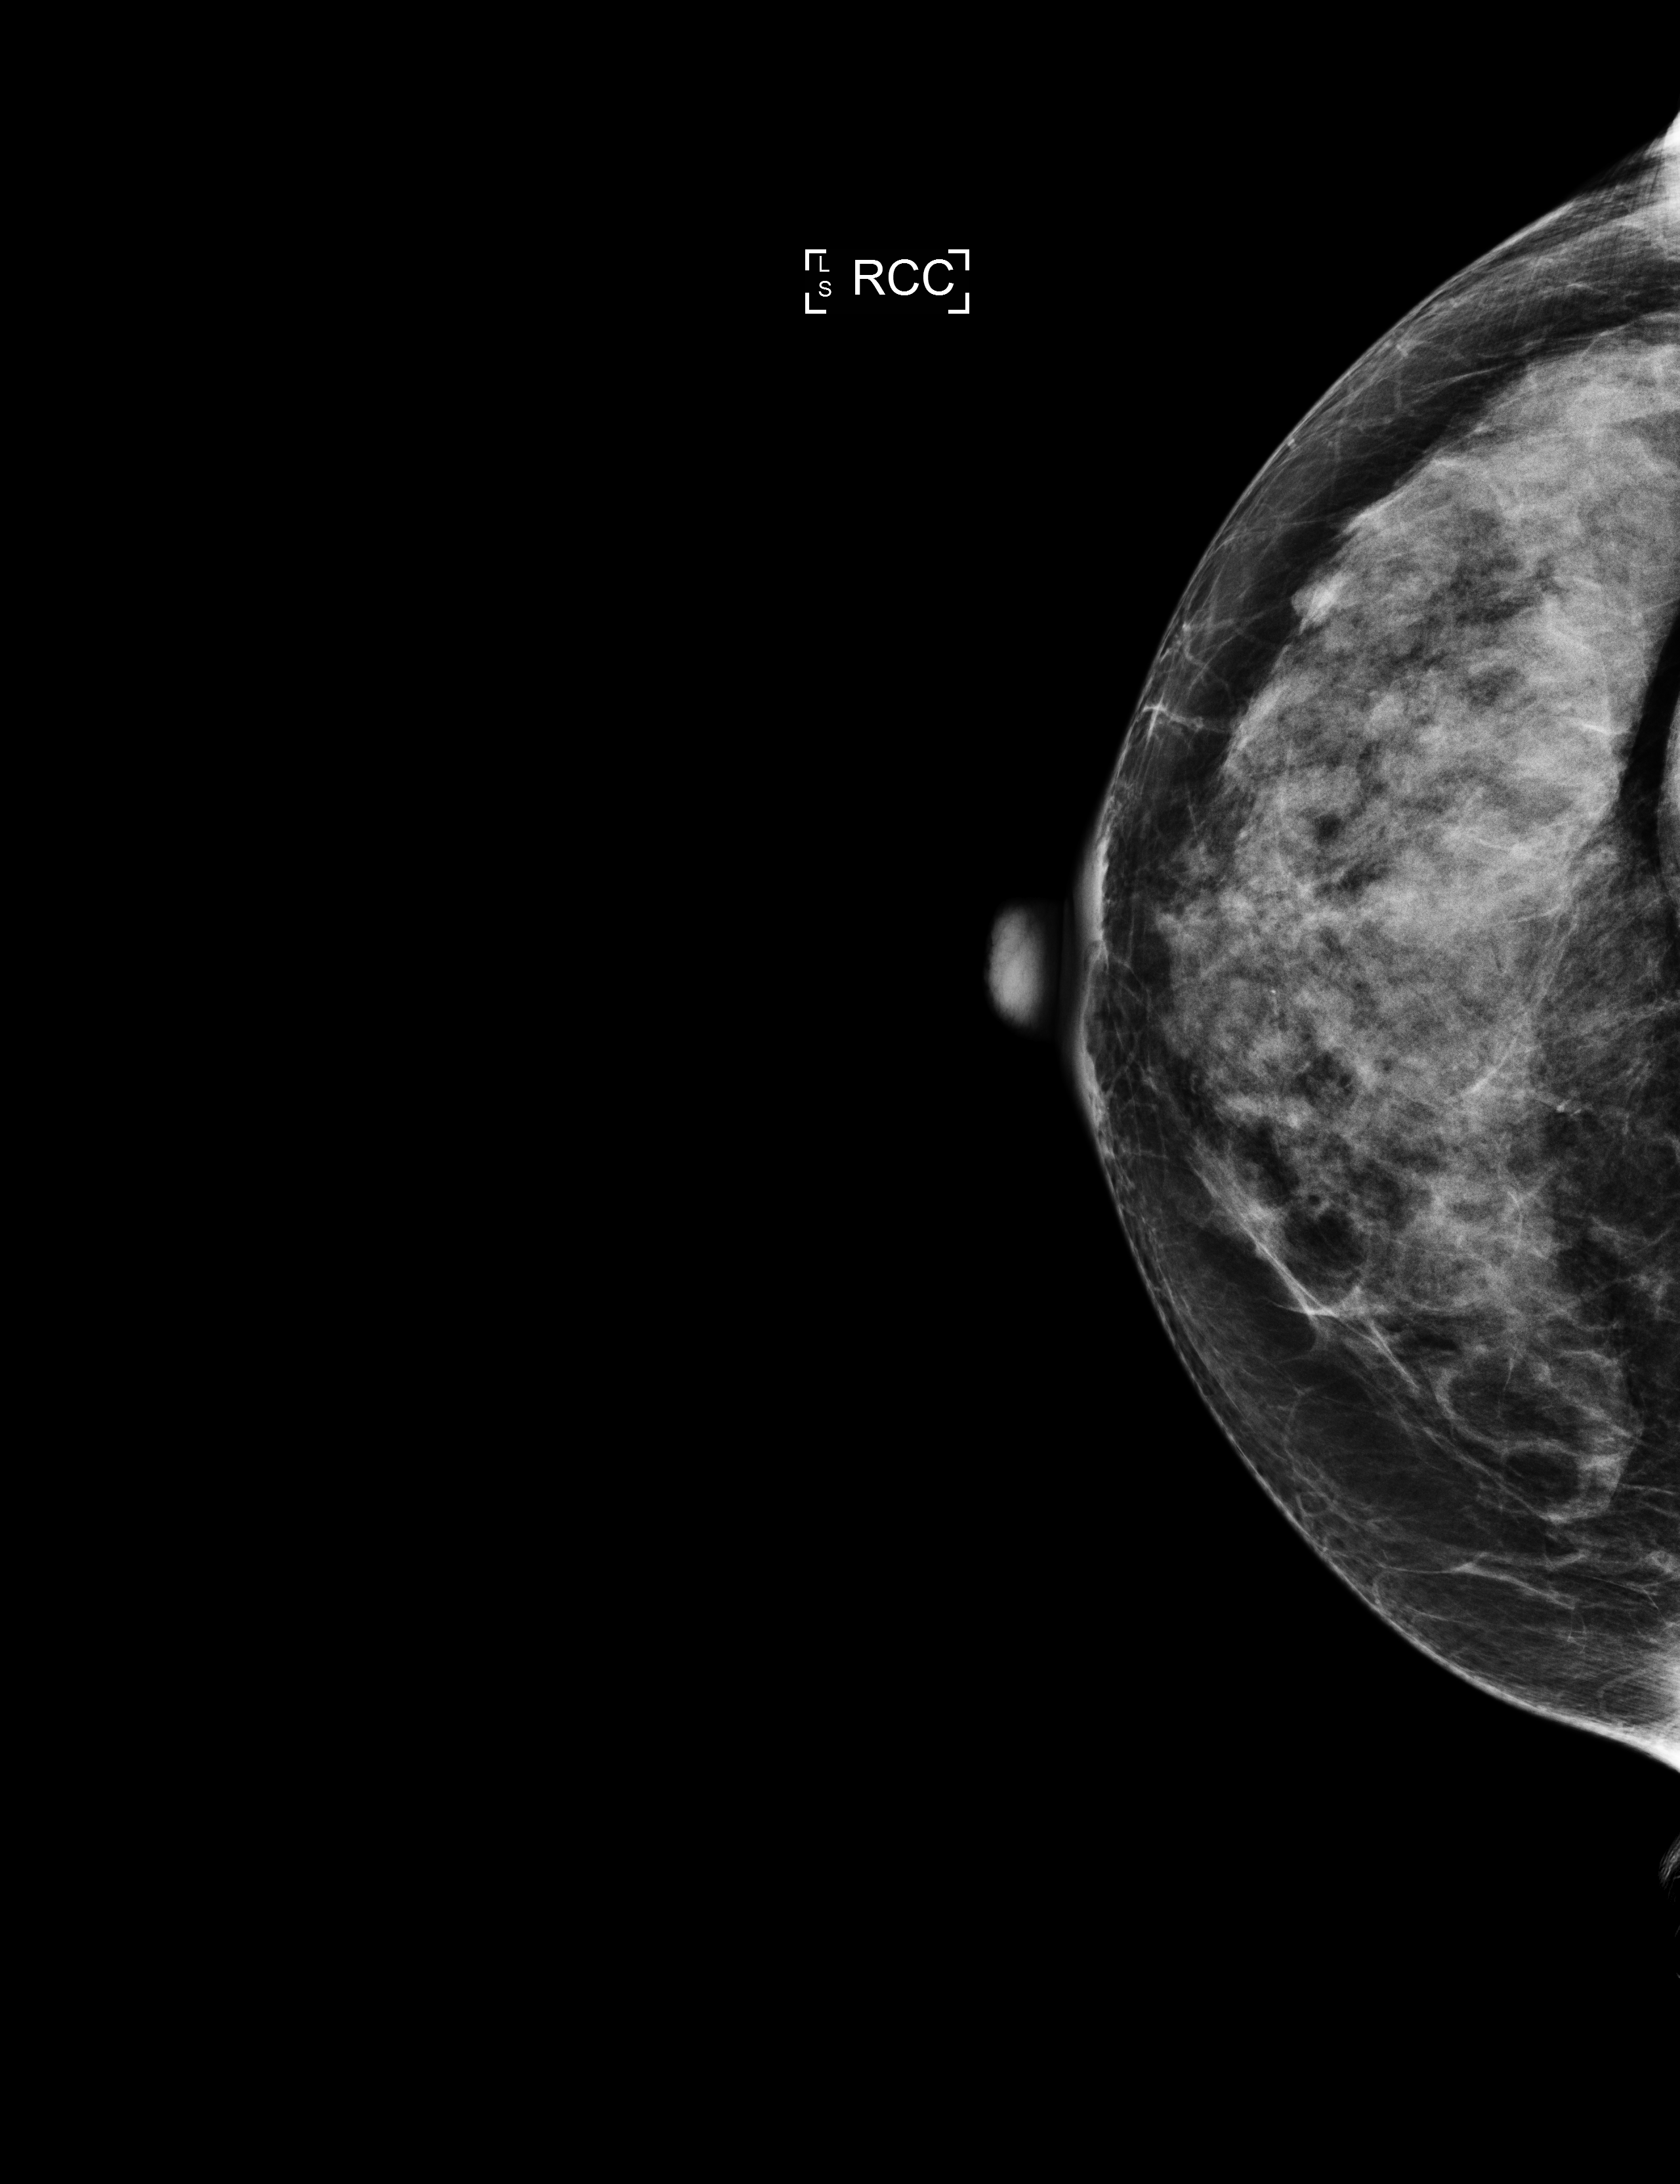
Screening examination. Patient: female, 68 years.
Image type: full-field digital mammogram. Breast: right. Projection: CC view.